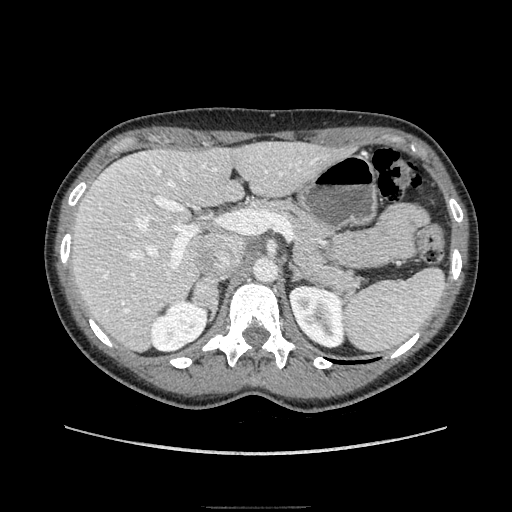
Contrast-enhanced abdominal CT, one axial slice. Slice 113 of 193 in the series (ordered by position). Soft-tissue window (W 400 / L 40 HU). 1.25 mm slice thickness. 512 × 512 image matrix, field of view 380 × 380 mm. Female patient. From the clinical record (not read from this slice): diagnosis: adrenocortical carcinoma; tumour side: right adrenal; tumour size at pathology: 3 cm; Ki-67 index: 4 %; stage (as recorded): 1.
Annotated regions visible in this slice (semi-automatically segmented with operator editing):
- mass: bounding box [x1, y1, x2, y2] px = [192, 276, 217, 319]